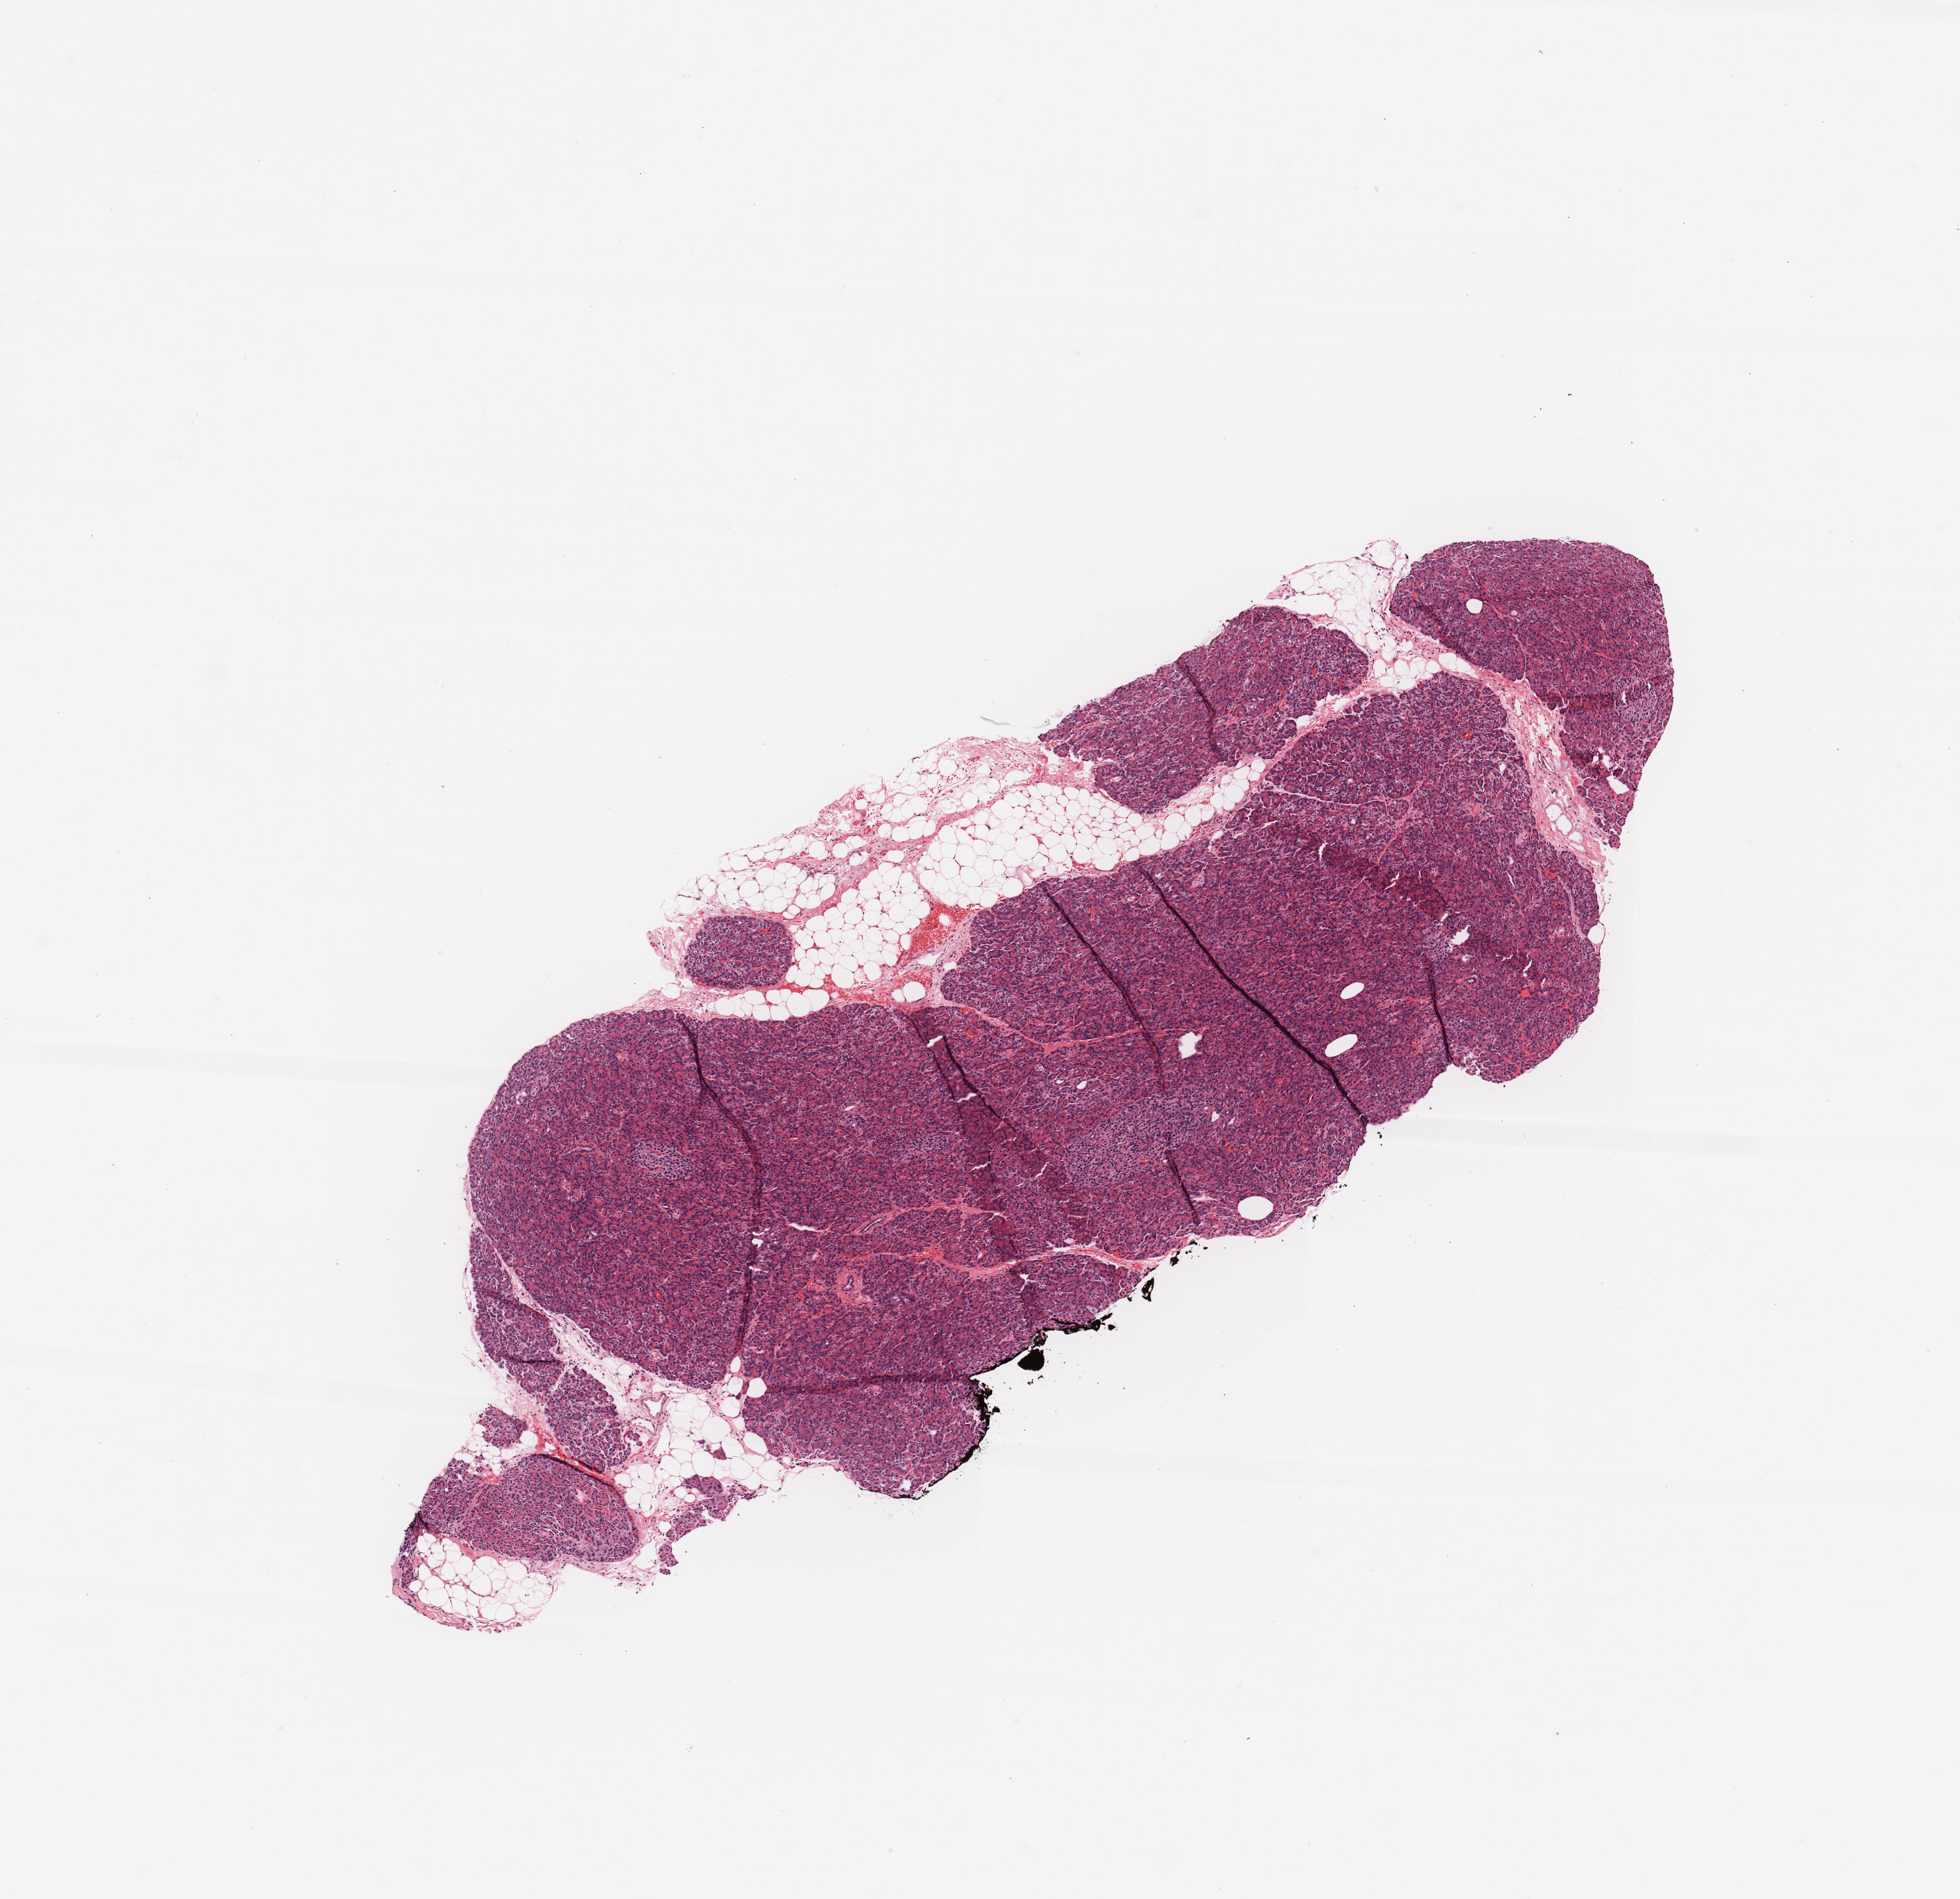
Digitized Hematoxylin and eosin (H&E) stained tissue section (whole slide), whole scanned area (about 5.9 x 5.7 mm) shown as a low-resolution overview. Normal (non-tumour) tissue sample, sampled site: pancreas. Patient: female, age 36 years.
This section: normal (non-tumour) tissue from the same patient. Patient diagnosis: Infiltrating duct carcinoma, NOS.